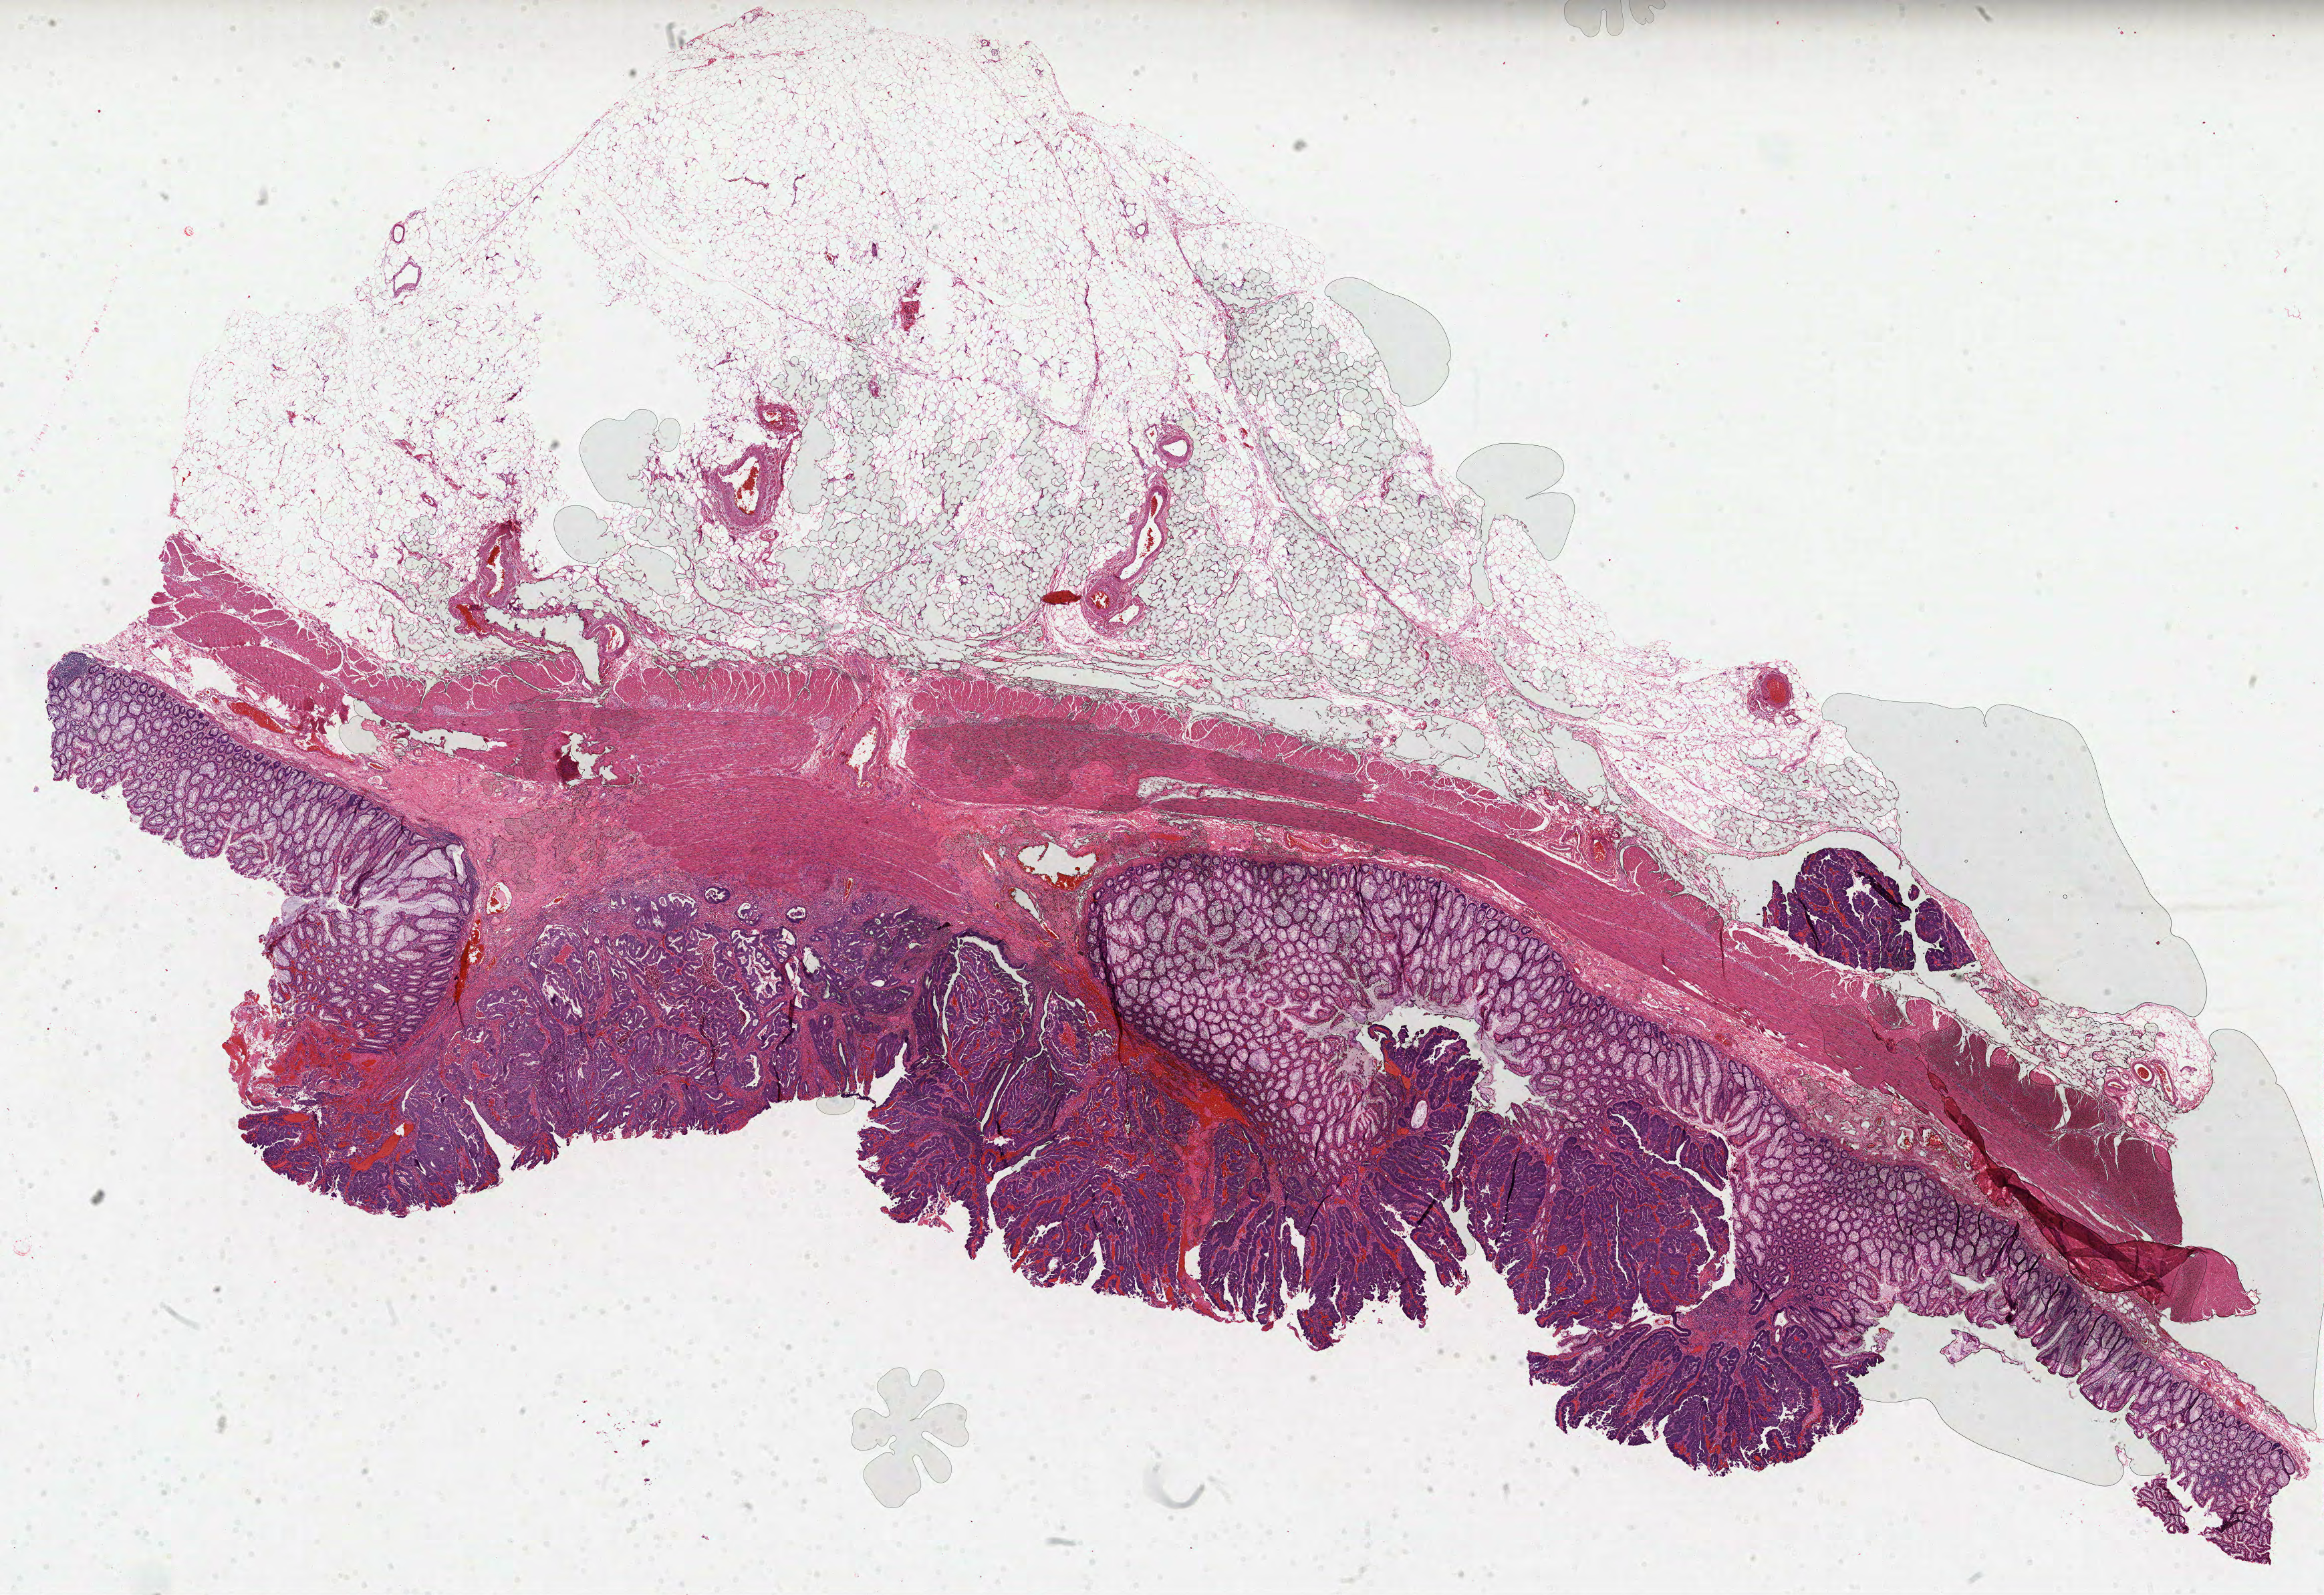
Whole-slide histology image, H&E, a low-resolution overview of the entire scanned area, about 28.0 x 19.2 mm (slide scanned at 40x), formalin-fixed paraffin-embedded (FFPE) diagnostic section, primary tumour sample from the colon. Male patient; age at initial diagnosis 61 years.
TNM: T3 N0 M1. AJCC pathologic stage: IVA. Lymph nodes positive (case pathology): 0 of 3 examined. Diagnosis: Adenocarcinoma, NOS (rectosigmoid junction).